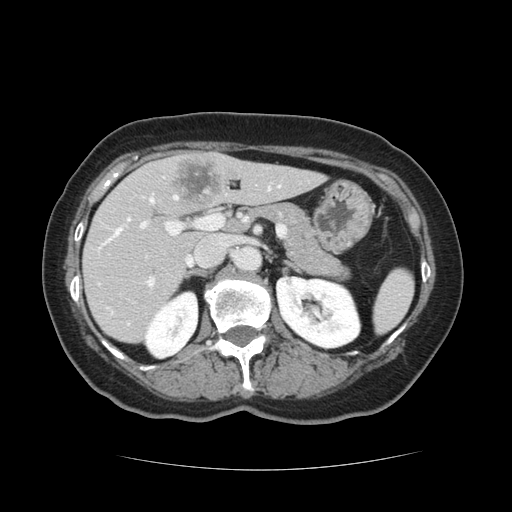
Contrast-enhanced abdominal CT, one axial slice. Position 67 of 128 along the scan axis. 120 kVp. Intravenous contrast given. Soft-tissue window (W 400 / L 40 HU). 2.5 mm slice thickness. 512 × 512 image matrix, field of view 366 × 366 mm. Female patient, age 67 years. From the clinical record (not read from this slice): diagnosis: colorectal cancer liver metastases, imaged before liver resection; multiple liver metastases: yes; largest metastasis: 3 cm; disease in both lobes: yes.
Annotated regions visible in this slice (expert manual segmentation):
- hepatic veins: bounding box (x1, y1, x2, y2) in pixels: (115, 196, 192, 264)
- liver: (84, 153, 322, 343)
- planned liver remnant (the part of the liver to remain after resection): (84, 163, 322, 343)
- portal vein (with intrahepatic branches): (140, 182, 273, 288)
- liver metastasis: (173, 160, 219, 205)